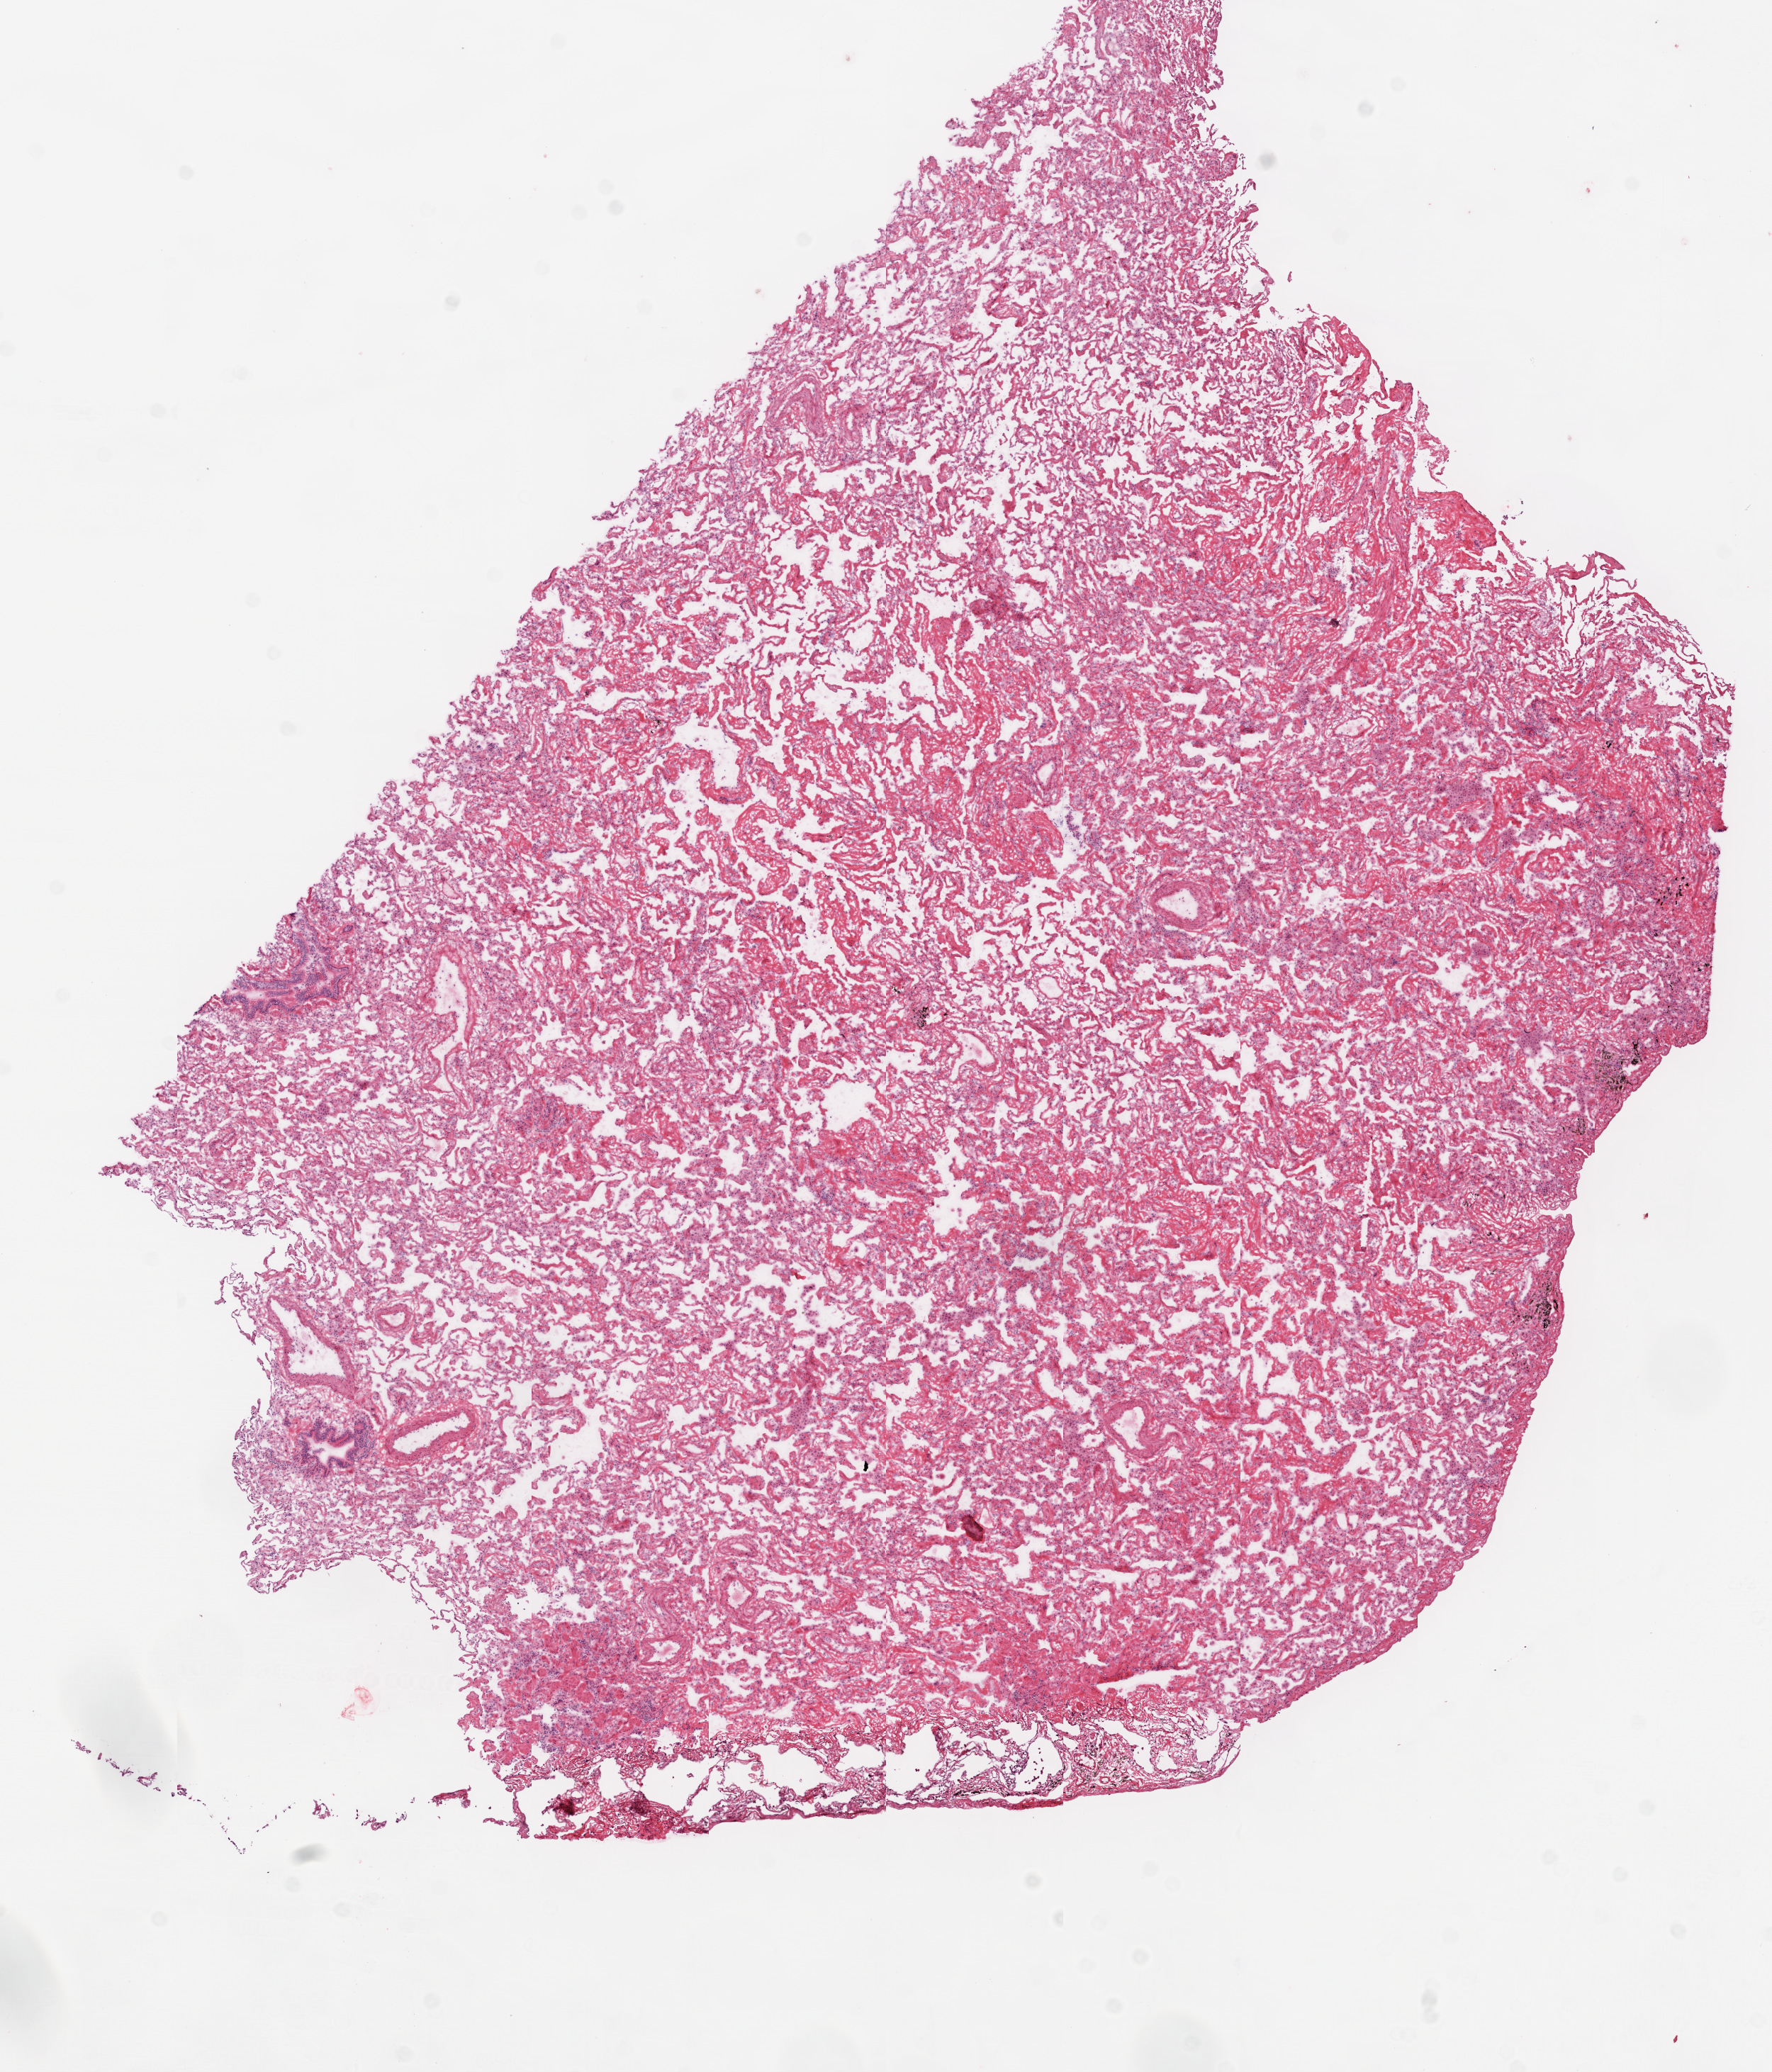
Hematoxylin and eosin (H&E) stained whole-slide image, low-resolution overview of the scanned area, about 10.0 x 11.7 mm, frozen section from the top of the tissue portion, lung, solid tissue normal (non-tumour tissue) sample. Female patient; age at initial diagnosis 73 years.
This section: solid tissue normal (non-tumour) sample from the same patient. Patient diagnosis: Squamous cell carcinoma, NOS (upper lobe, lung).